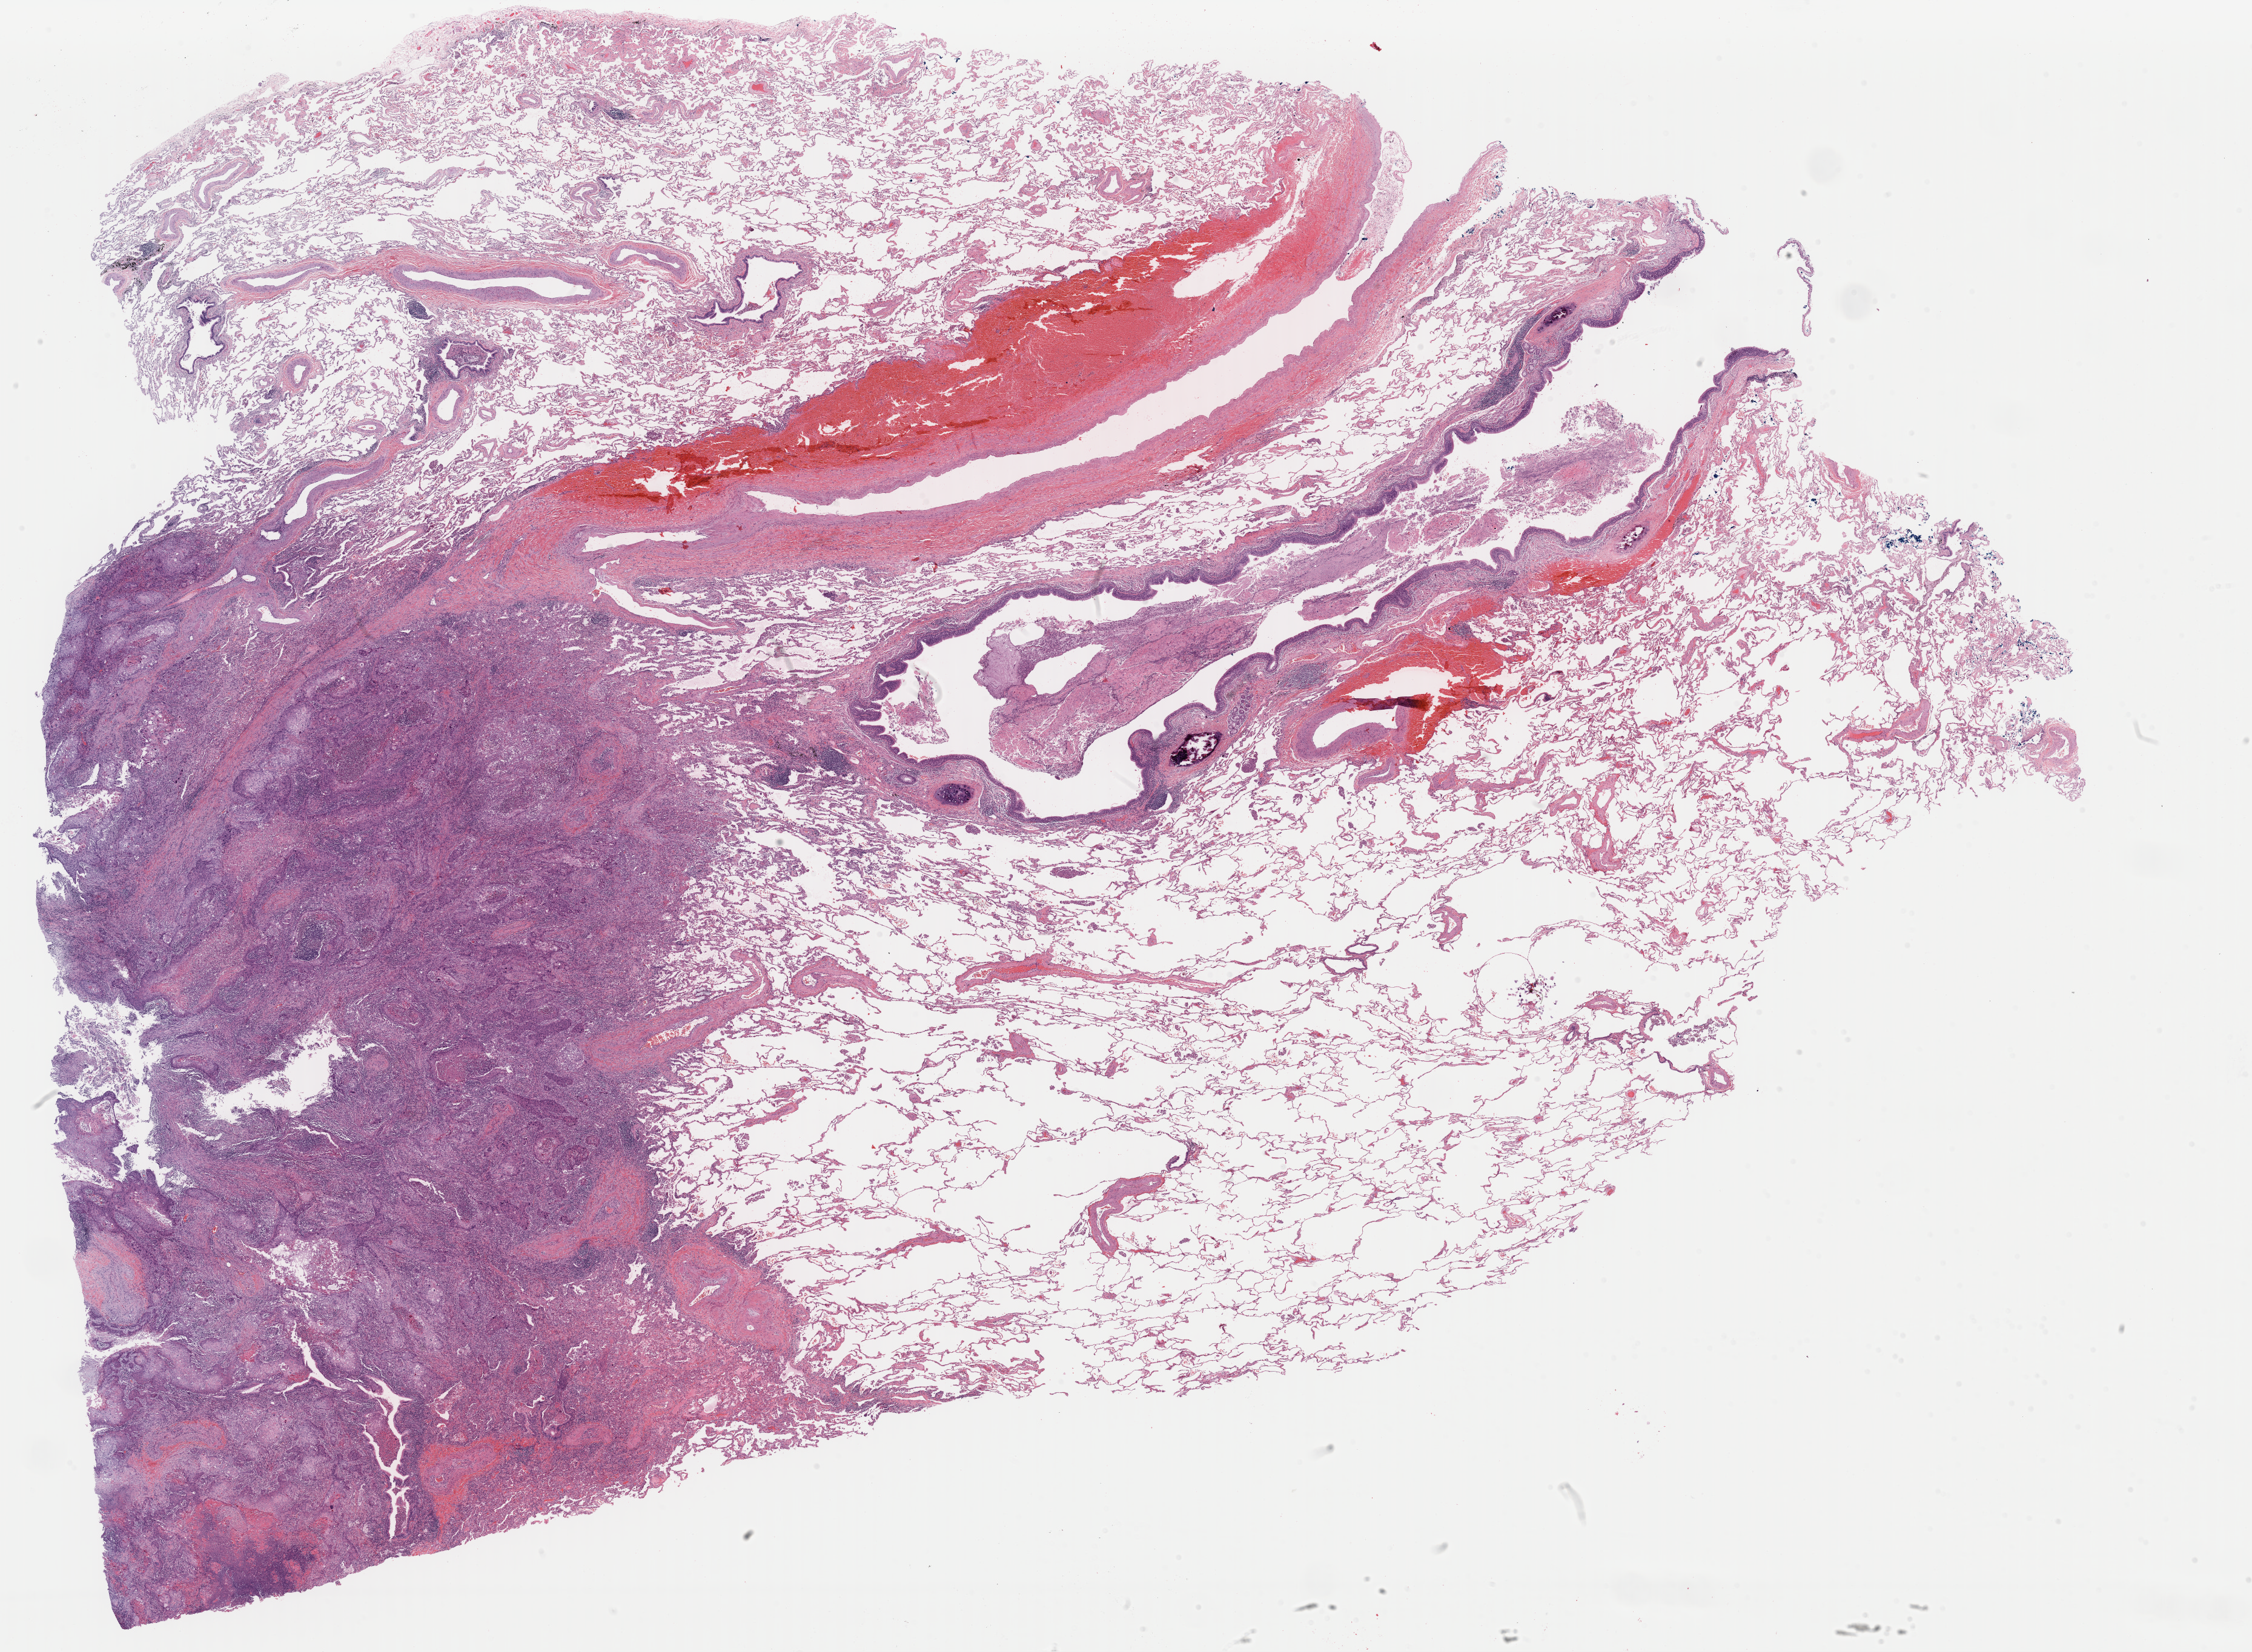
Digitized H&E tissue section (whole slide), whole scanned area (about 29.4 x 21.5 mm) shown as a low-resolution overview, formalin-fixed paraffin-embedded (FFPE) diagnostic section, lung, primary tumour sample. Patient sex: male.
Pathologic diagnosis: Squamous cell carcinoma, keratinizing, NOS (upper lobe, lung). Laterality: left. AJCC pathologic stage: IB (7th edition).